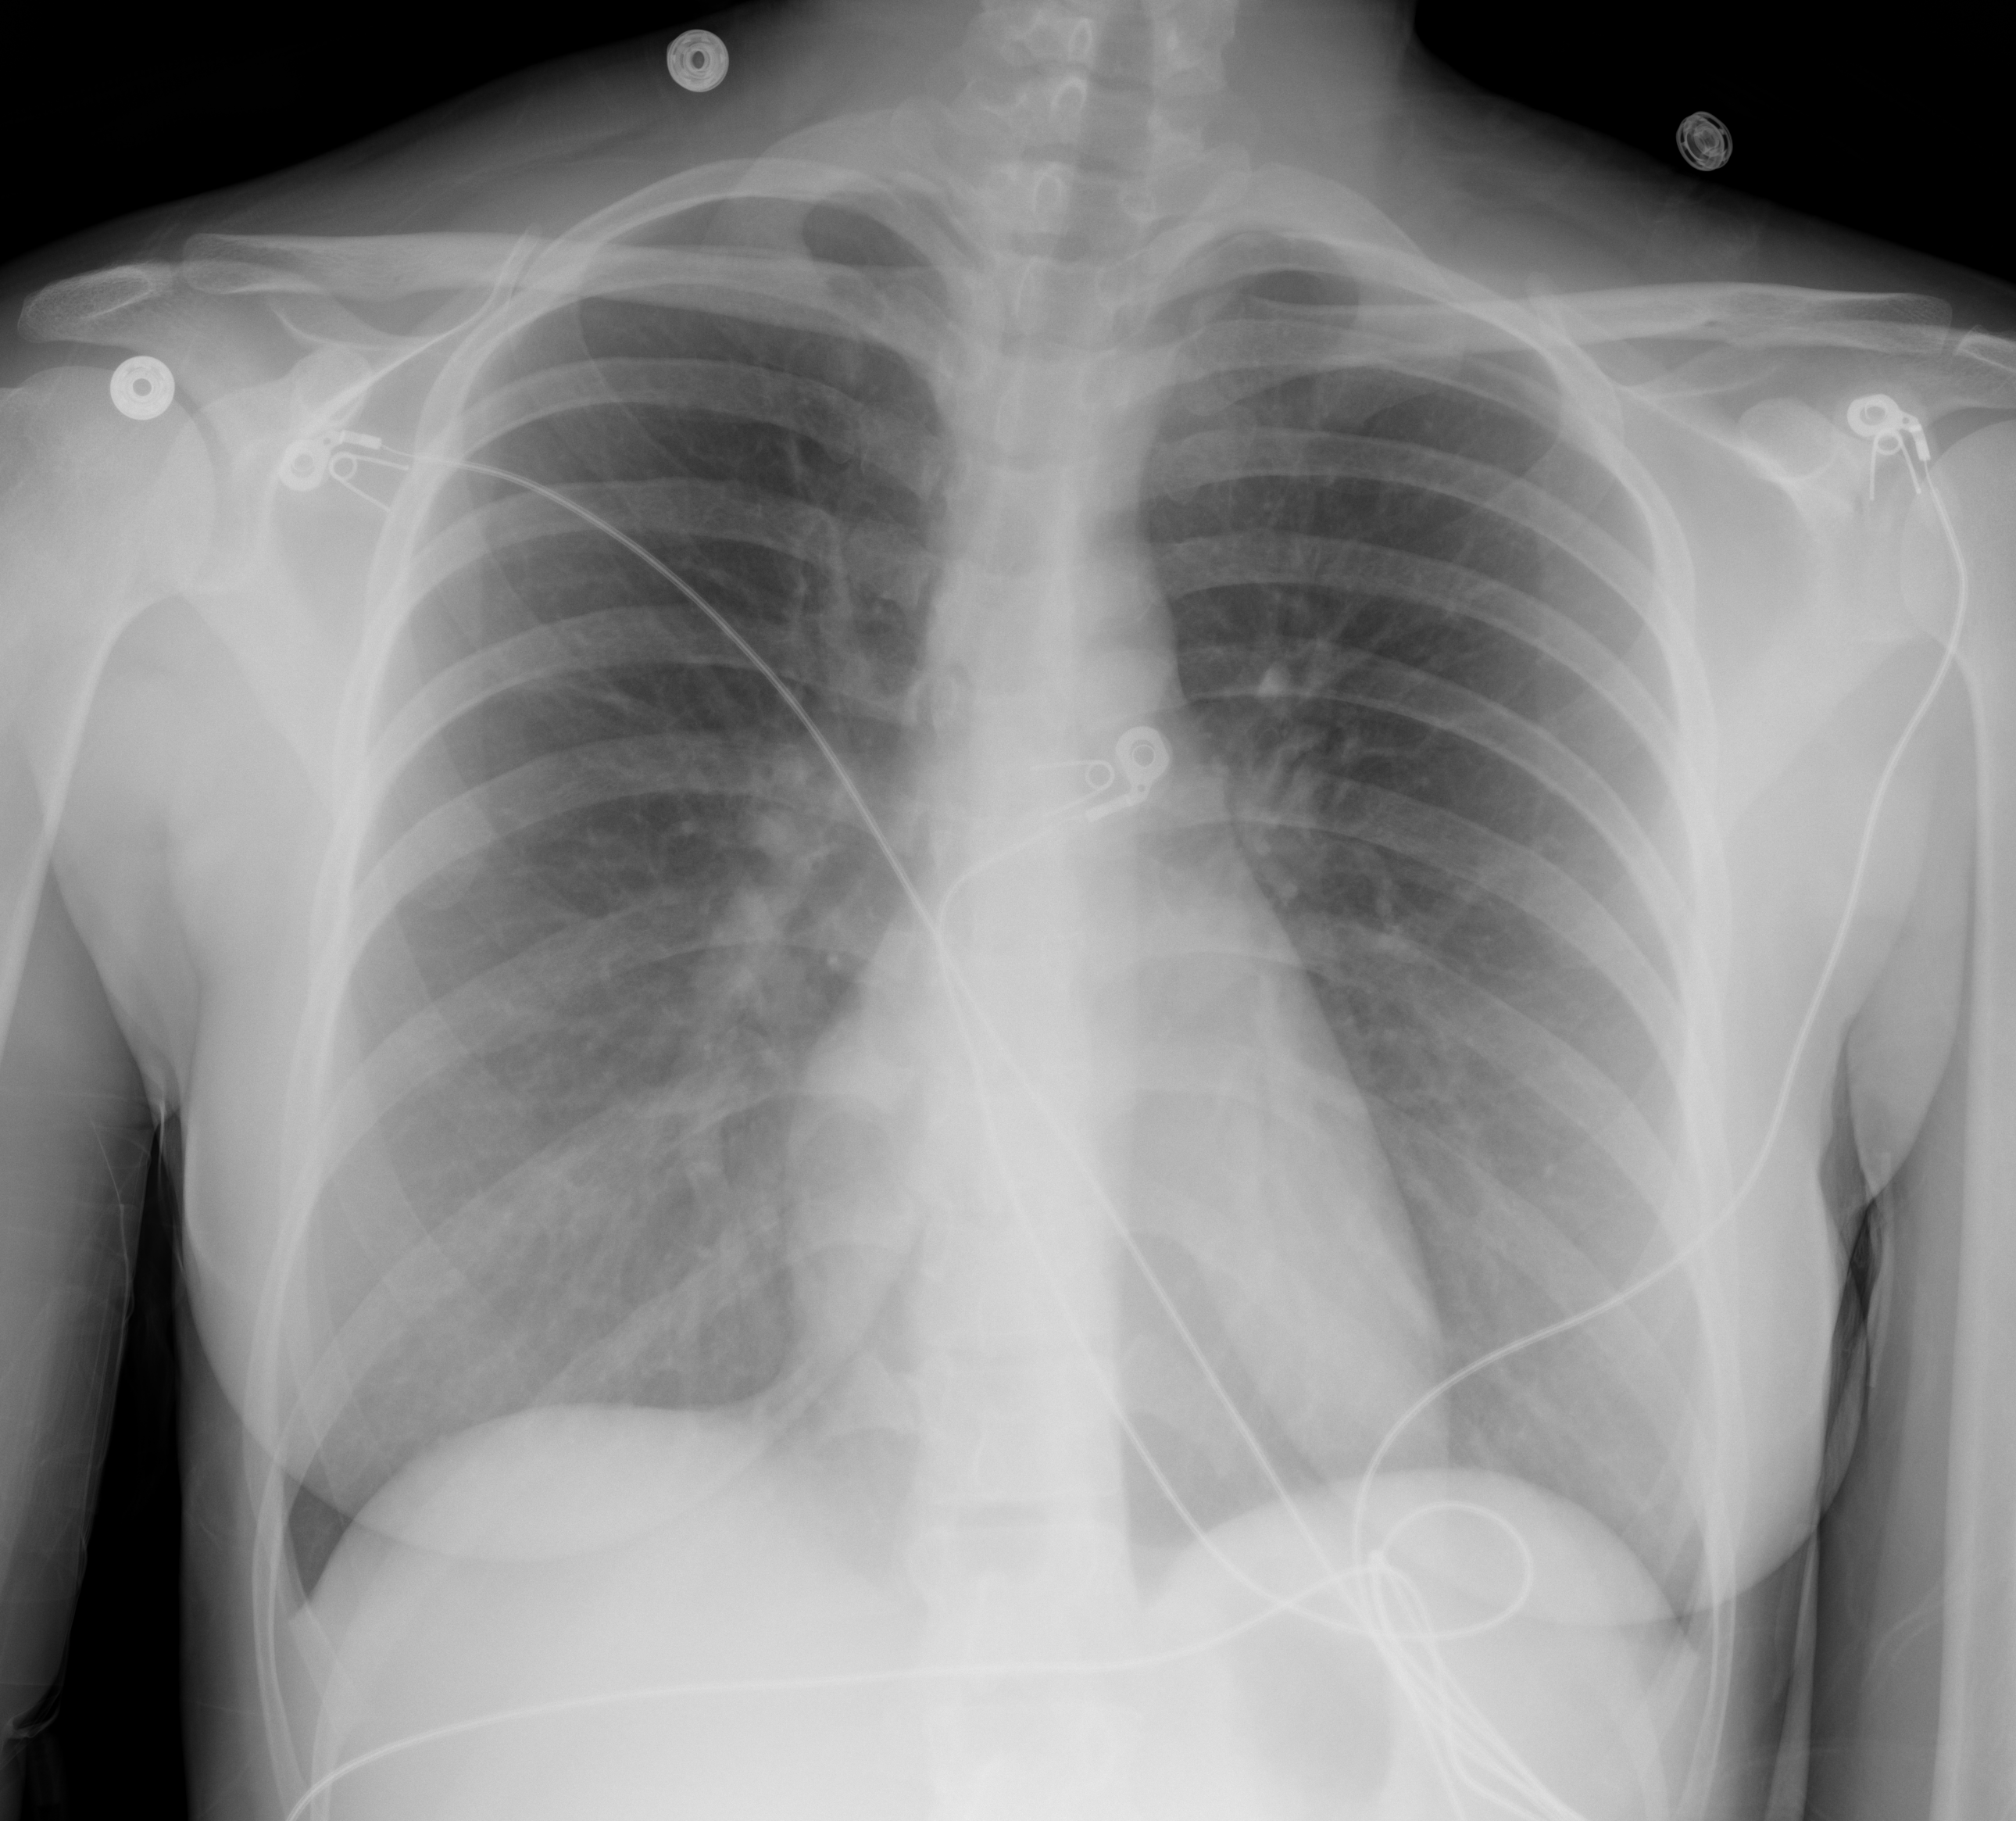
Chest X-ray (portable), AP projection. Female patient, age 29 years; COVID-19 (test-positive).
Key findings recorded by the radiologist: The lungs are clear and without focal consolidation.